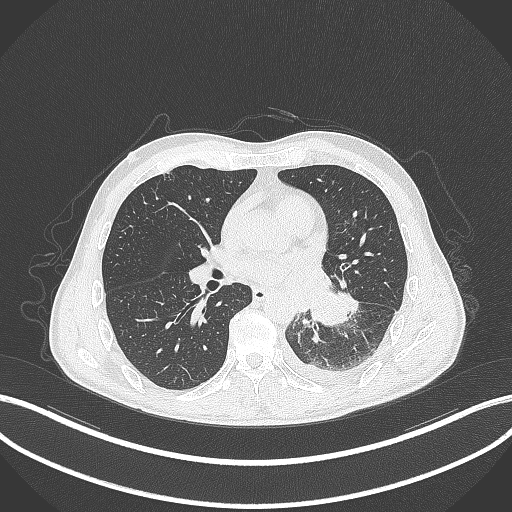
Chest CT, one axial slice. Position 154 of 295 along the scan axis. 120 kVp. Lung window (W 1500 / L -600 HU). 512 × 512 image matrix. Male patient, age 47 years. Case-level facts recorded for this patient, not image findings: clinical TNM (as recorded): T3 N1 M1c; histopathological grade: G3.
Annotated regions visible in this slice (bounding box drawn by a radiologist):
- lung tumour (recorded histology: small cell carcinoma): bounding box (x1, y1, x2, y2) in pixels: (310, 289, 352, 327)